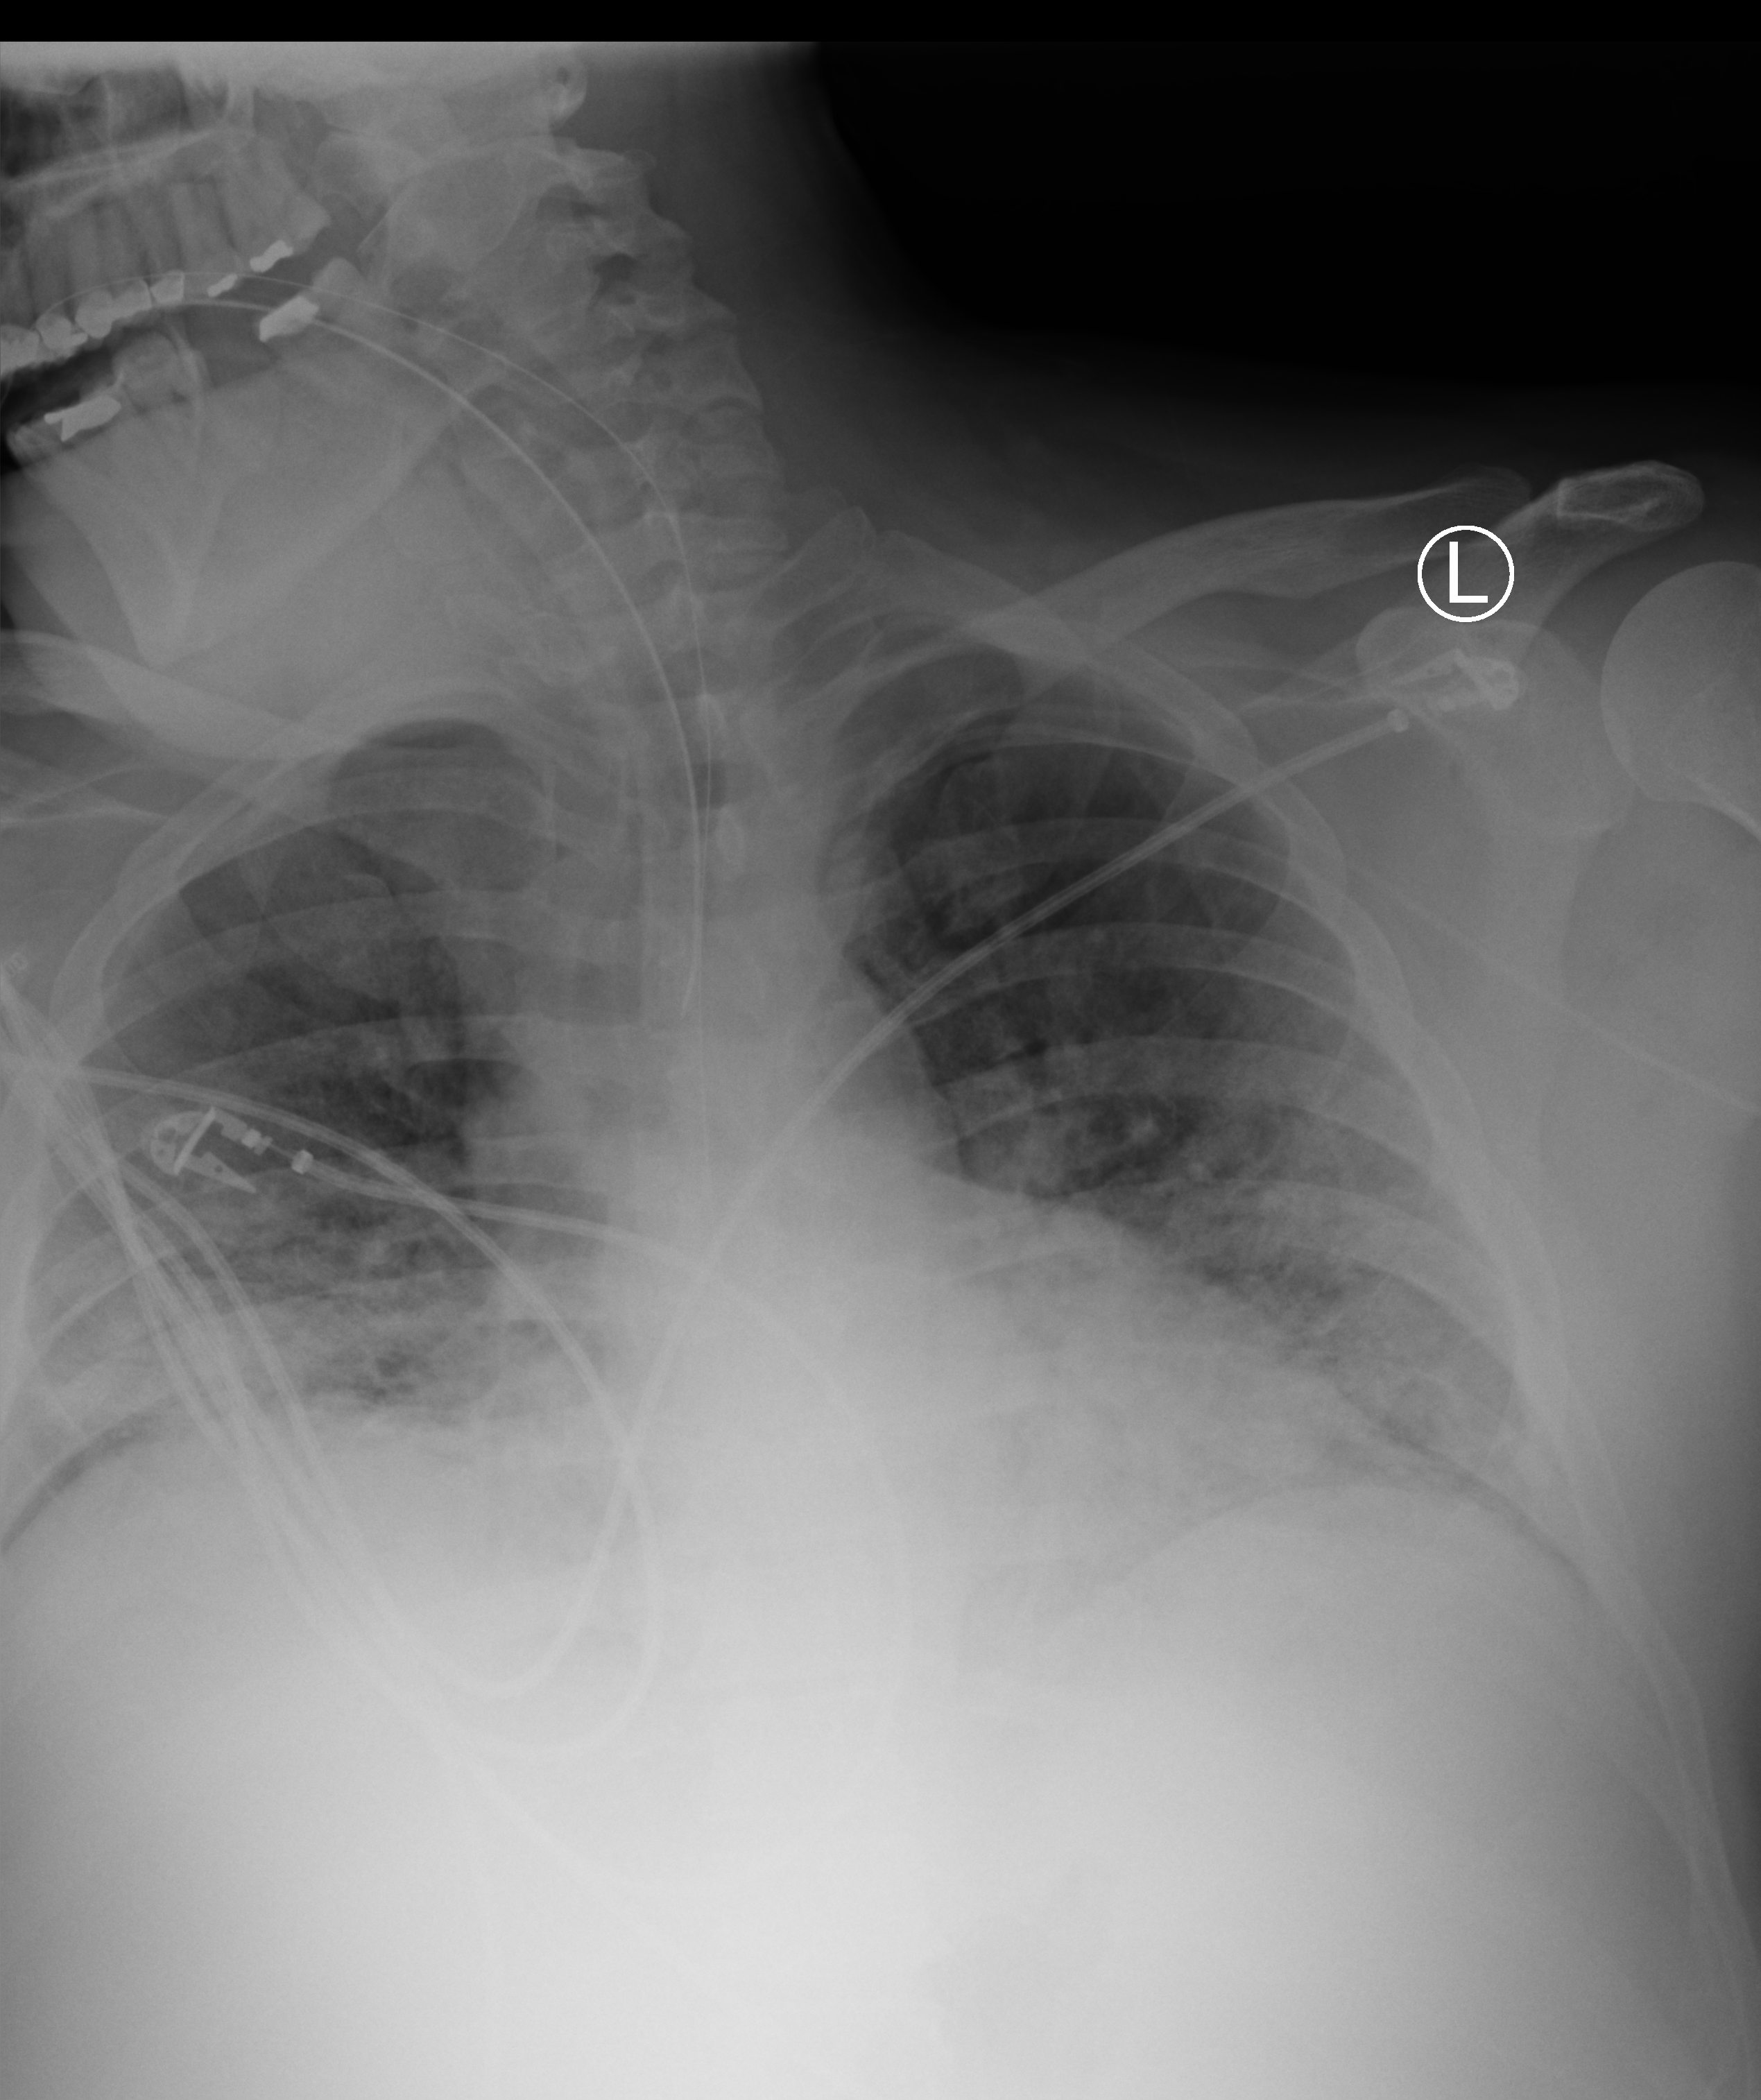
Chest X-ray (portable), anteroposterior (AP) projection. Patient hospitalised with COVID-19; male, aged 18–59 years.
Hospital-stay facts (about this admission, not read from this image; timing relative to this image not recorded): mechanically ventilated during this hospital stay: yes; other chronic lung disease (admission record): no.